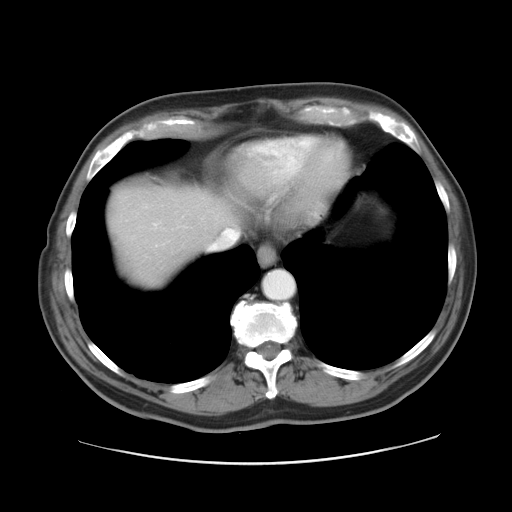
Contrast-enhanced abdominal CT, one axial slice. Position 25 of 28 along the scan axis. 120 kVp. Intravenous contrast given. Soft-tissue window (W 400 / L 40 HU). 512 × 512 image matrix, field of view 402 × 402 mm. Male patient, age 74 years. From the clinical record (not read from this slice): diagnosis: colorectal cancer liver metastases, imaged before liver resection; multiple liver metastases: no; largest metastasis: 5 cm.
Annotated regions visible in this slice (manually delineated by an expert):
- hepatic veins: bounding box [x1, y1, x2, y2] px = [210, 229, 240, 250]
- liver: [111, 189, 232, 284]
- planned liver remnant (the part of the liver to remain after resection): [111, 190, 210, 284]